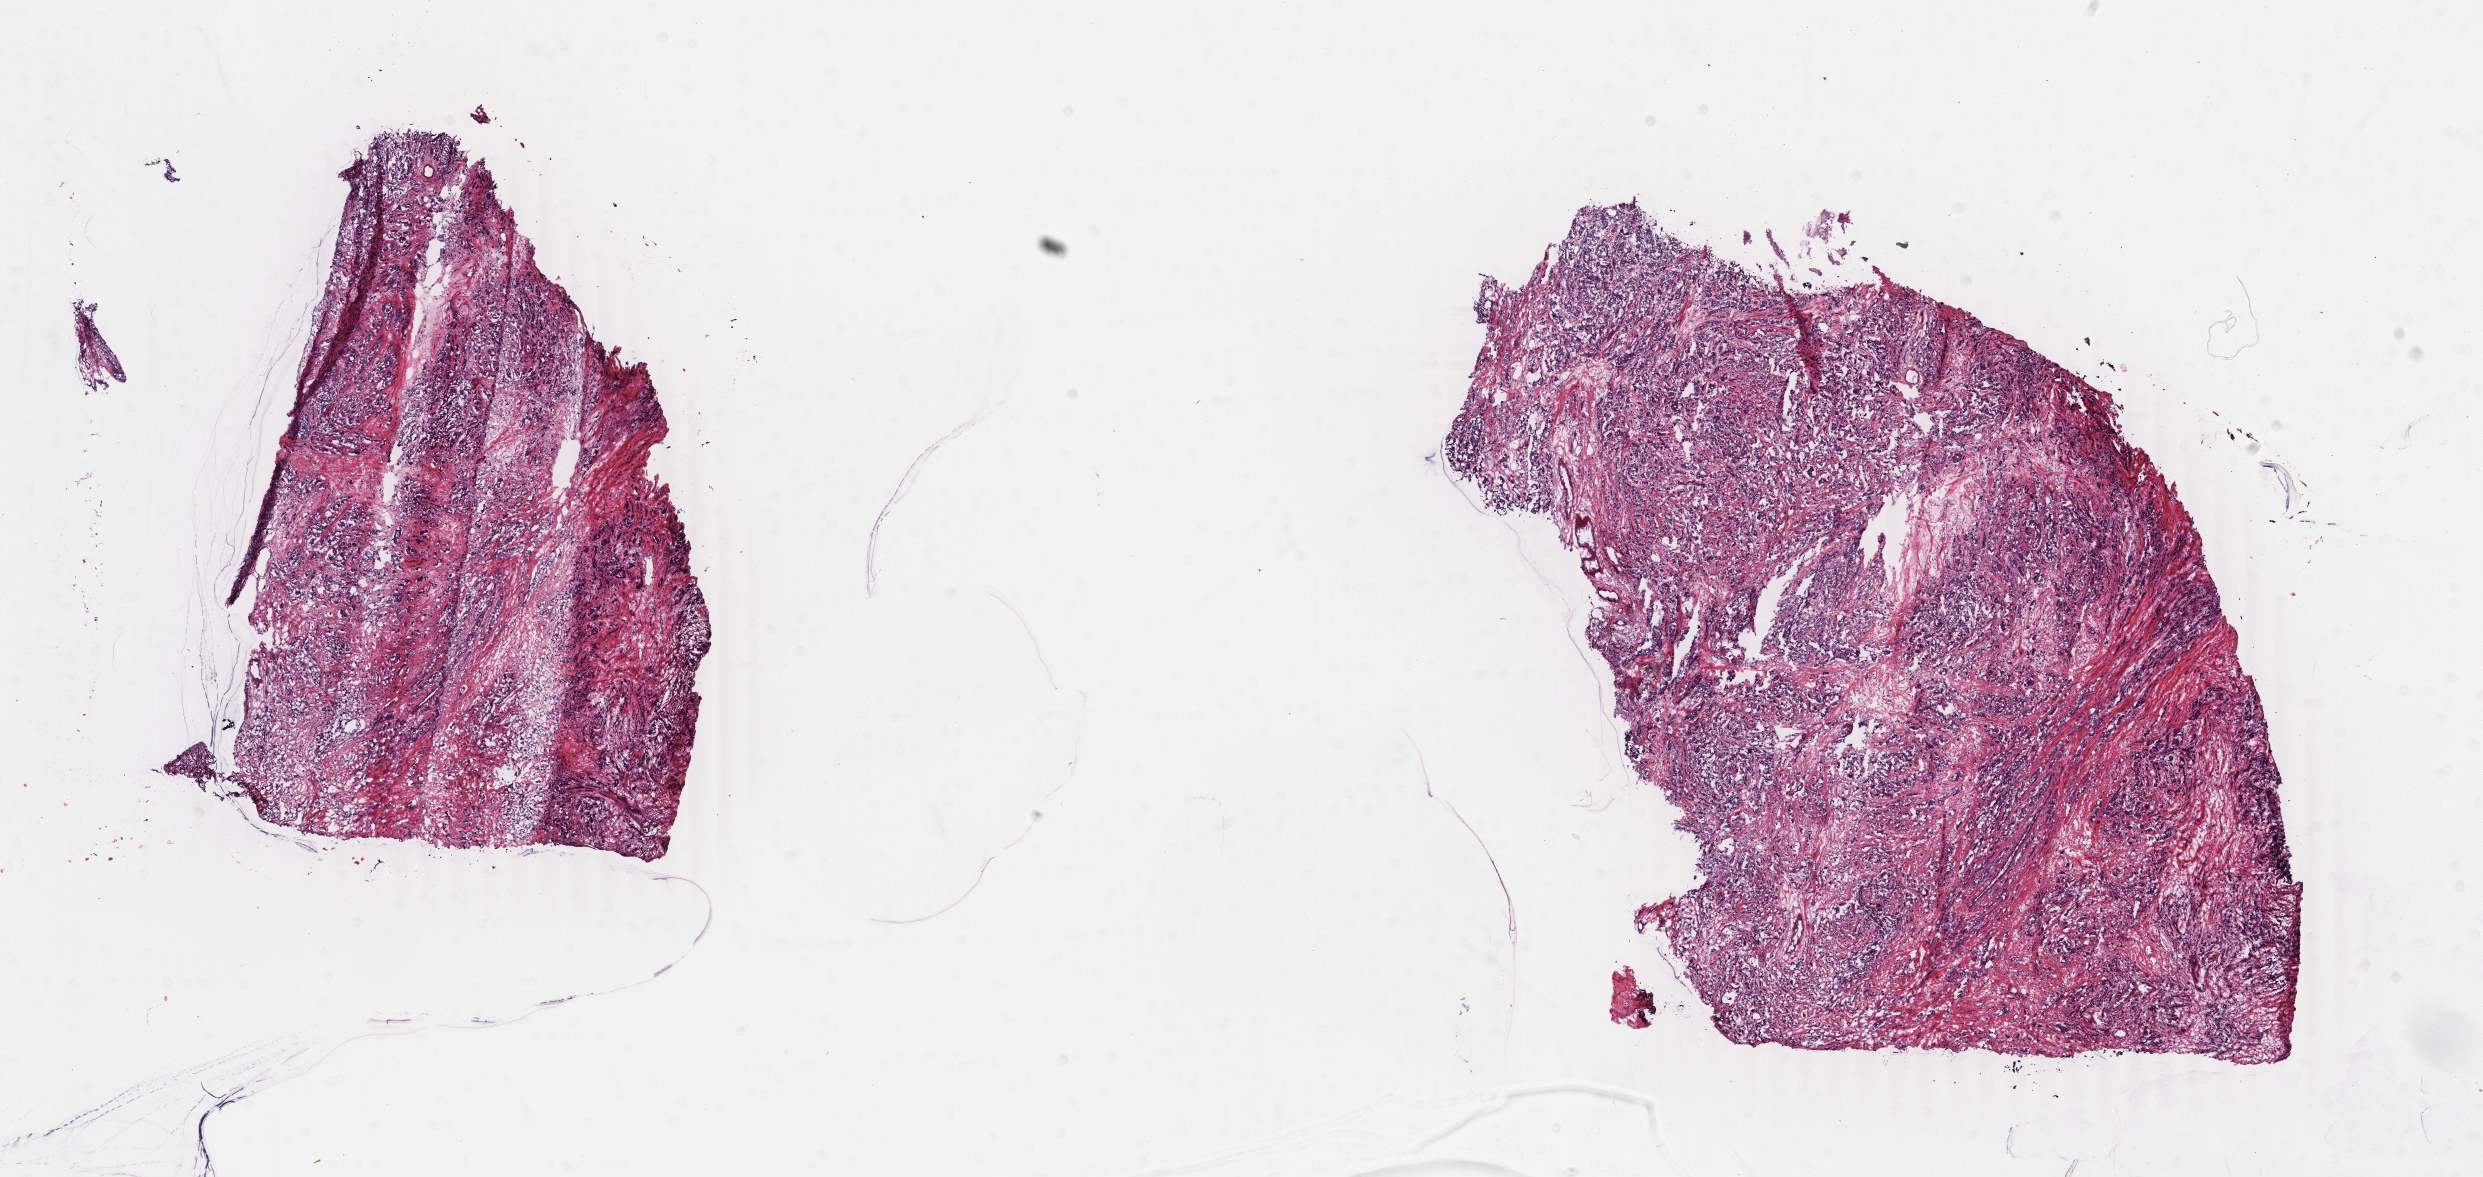
Digitized H&E-stained tissue section (whole slide), shown as a low-resolution overview of the whole scanned area (about 19.8 x 9.4 mm, from a 40x scan); frozen section from the top of the tissue portion; breast, primary tumour sample. Female patient; age at initial diagnosis 44 years. Slide review estimates, as recorded: tumour cells 100%, tumour nuclei 80%, normal cells 0%, stromal cells 0%, necrosis 0%. Inflammatory infiltration, as recorded: lymphocyte infiltration 0%, monocyte infiltration 0%, neutrophil infiltration 0%.
AJCC pathologic stage: IIIA. Lymph nodes positive (case pathology): 3 of 11 examined. Laterality: right. Histologic diagnosis: Infiltrating duct carcinoma, NOS.